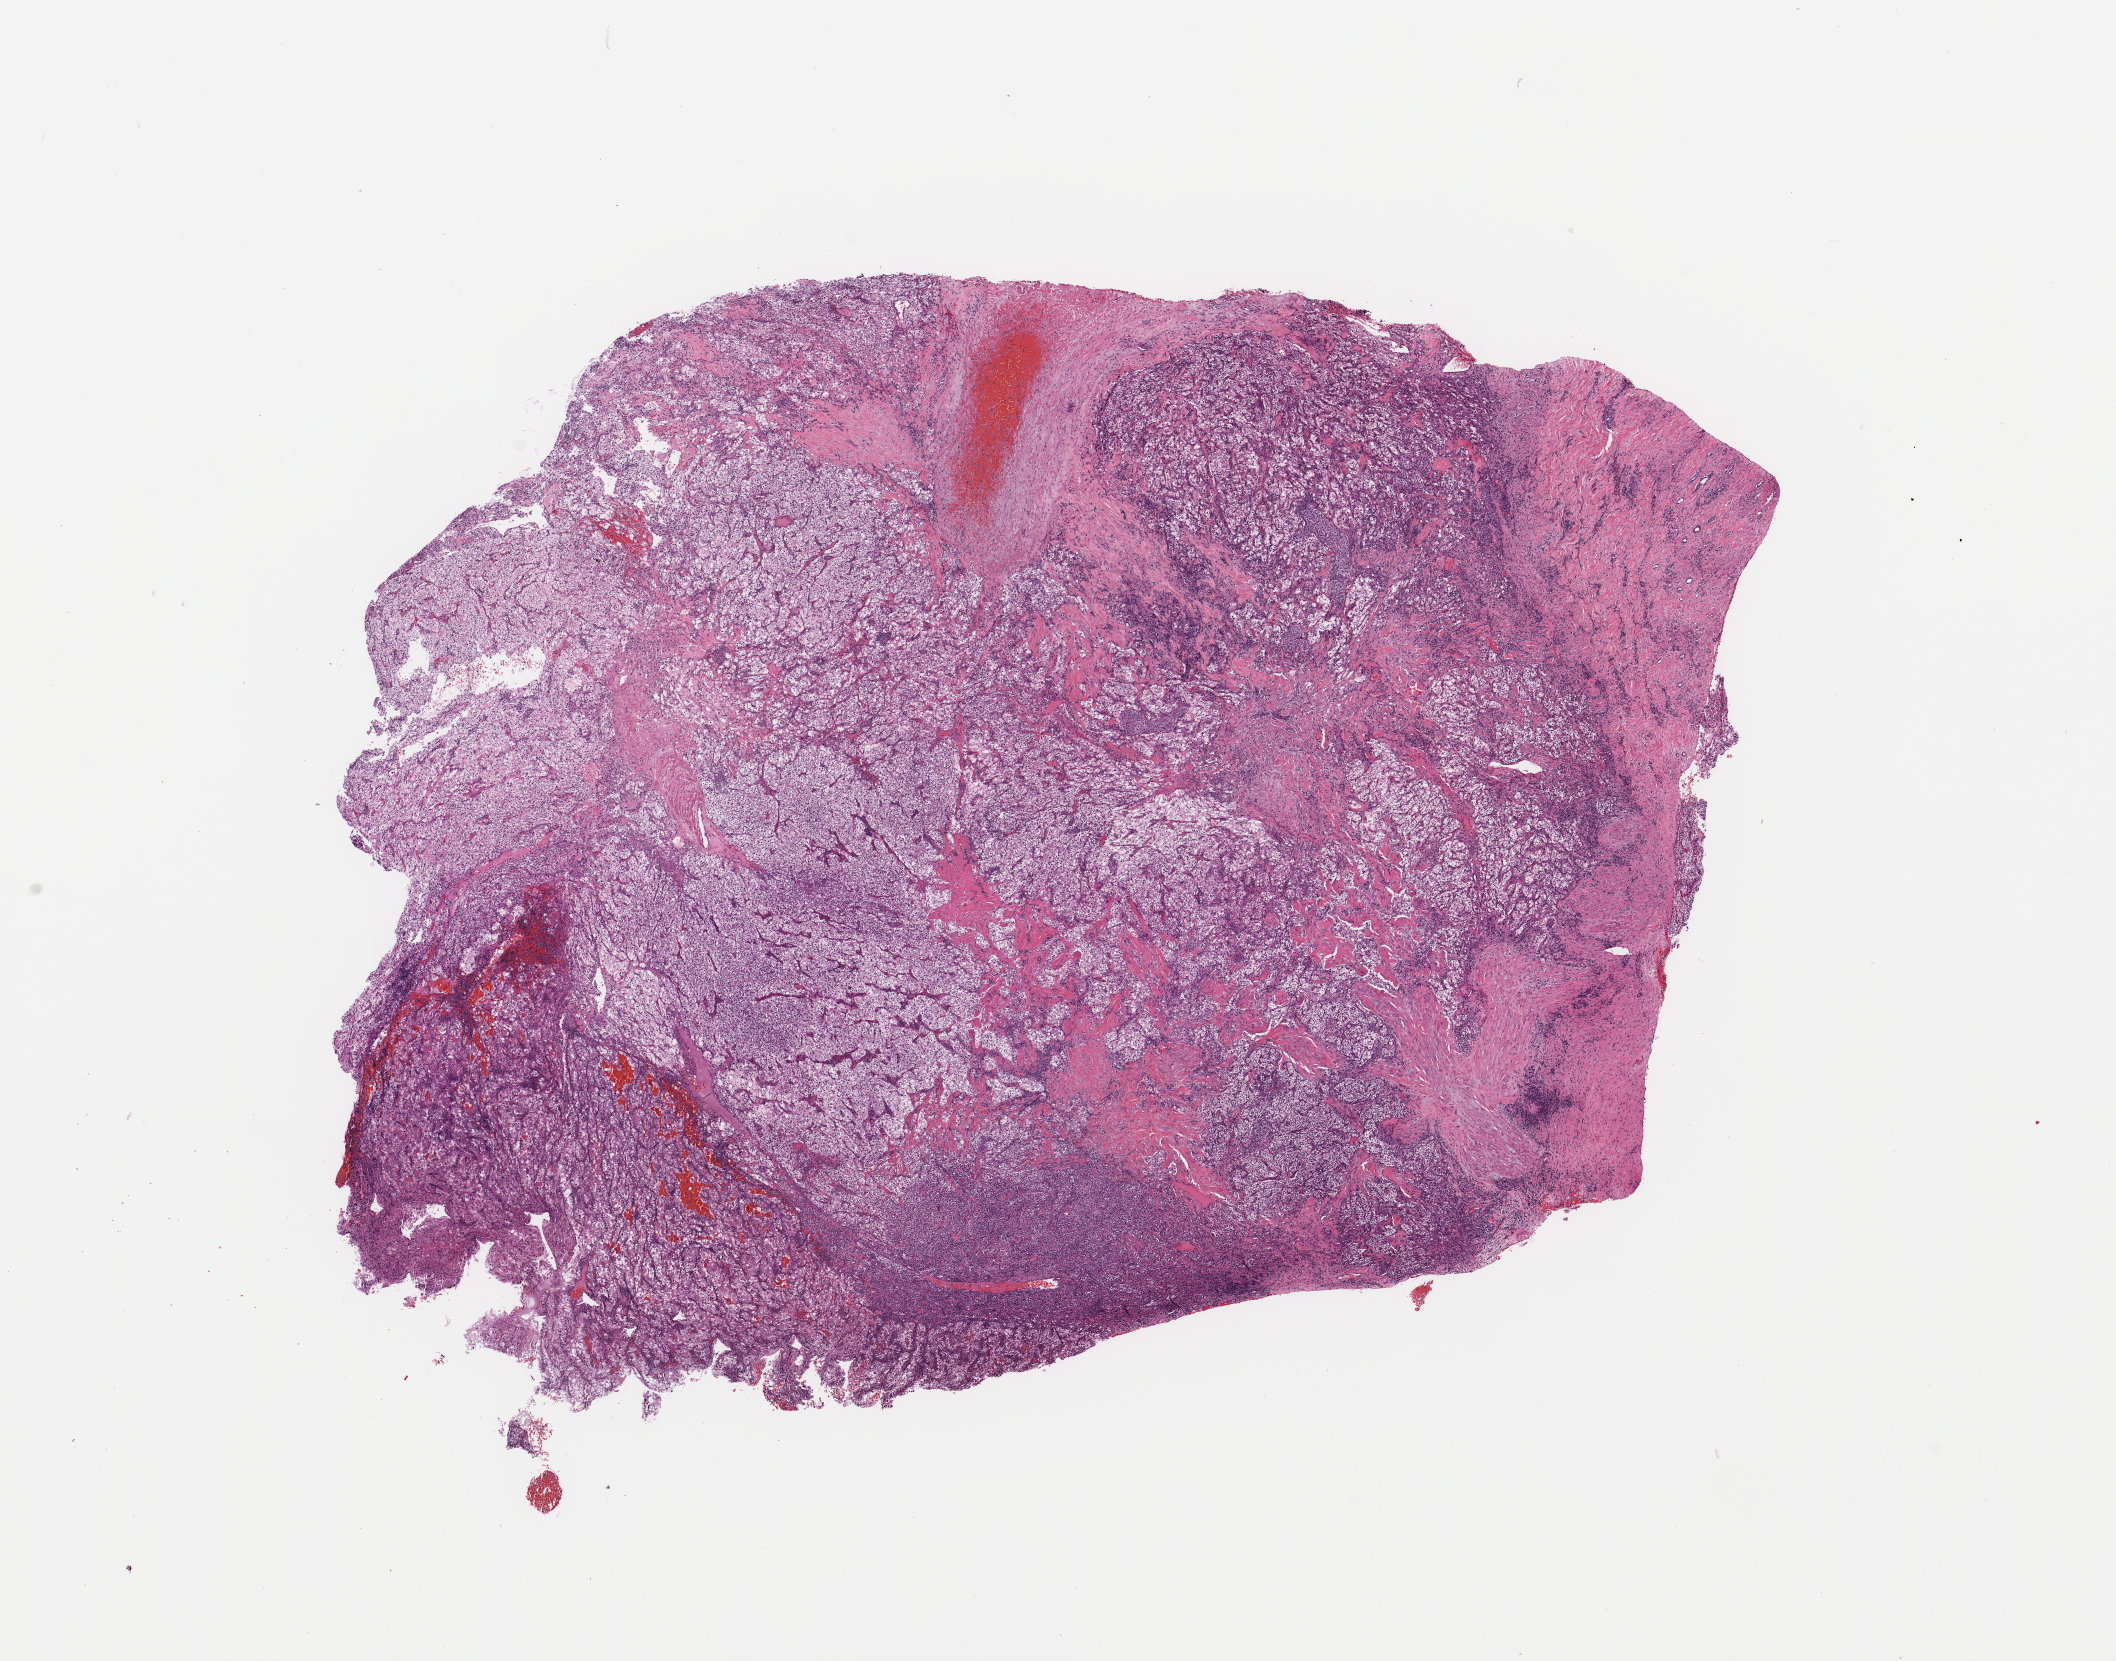
Whole-slide histology image, H&E-stained — low-resolution overview of the scanned area, about 16.7 x 13.1 mm (from a 20x scan); kidney, tumour tissue. 40-year-old male patient. Histologic grade: G3 (poorly differentiated).
Diagnosis: Renal cell carcinoma, NOS. AJCC pathologic stage: IV.